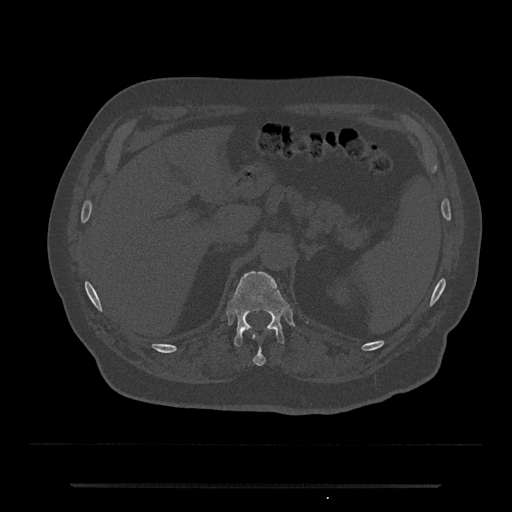
CT including the spine, one axial slice; slice 610 of 797 in the series (ordered by position); bone window (W 1800 / L 400 HU); 0.5 mm slice thickness; 512 × 512 image matrix, field of view 434 × 434 mm. Patient: male, 80 years. Case-level facts recorded for this patient, not image findings: primary cancer: prostate; vertebrae with lytic lesions (as recorded): L1, T11.
Annotated regions visible in this slice (semi-automatically segmented with operator editing):
- T11 vertebra: bounding box <253,335,266,366> (left, top, right, bottom; pixels)
- T12 vertebra: <228,271,289,346>